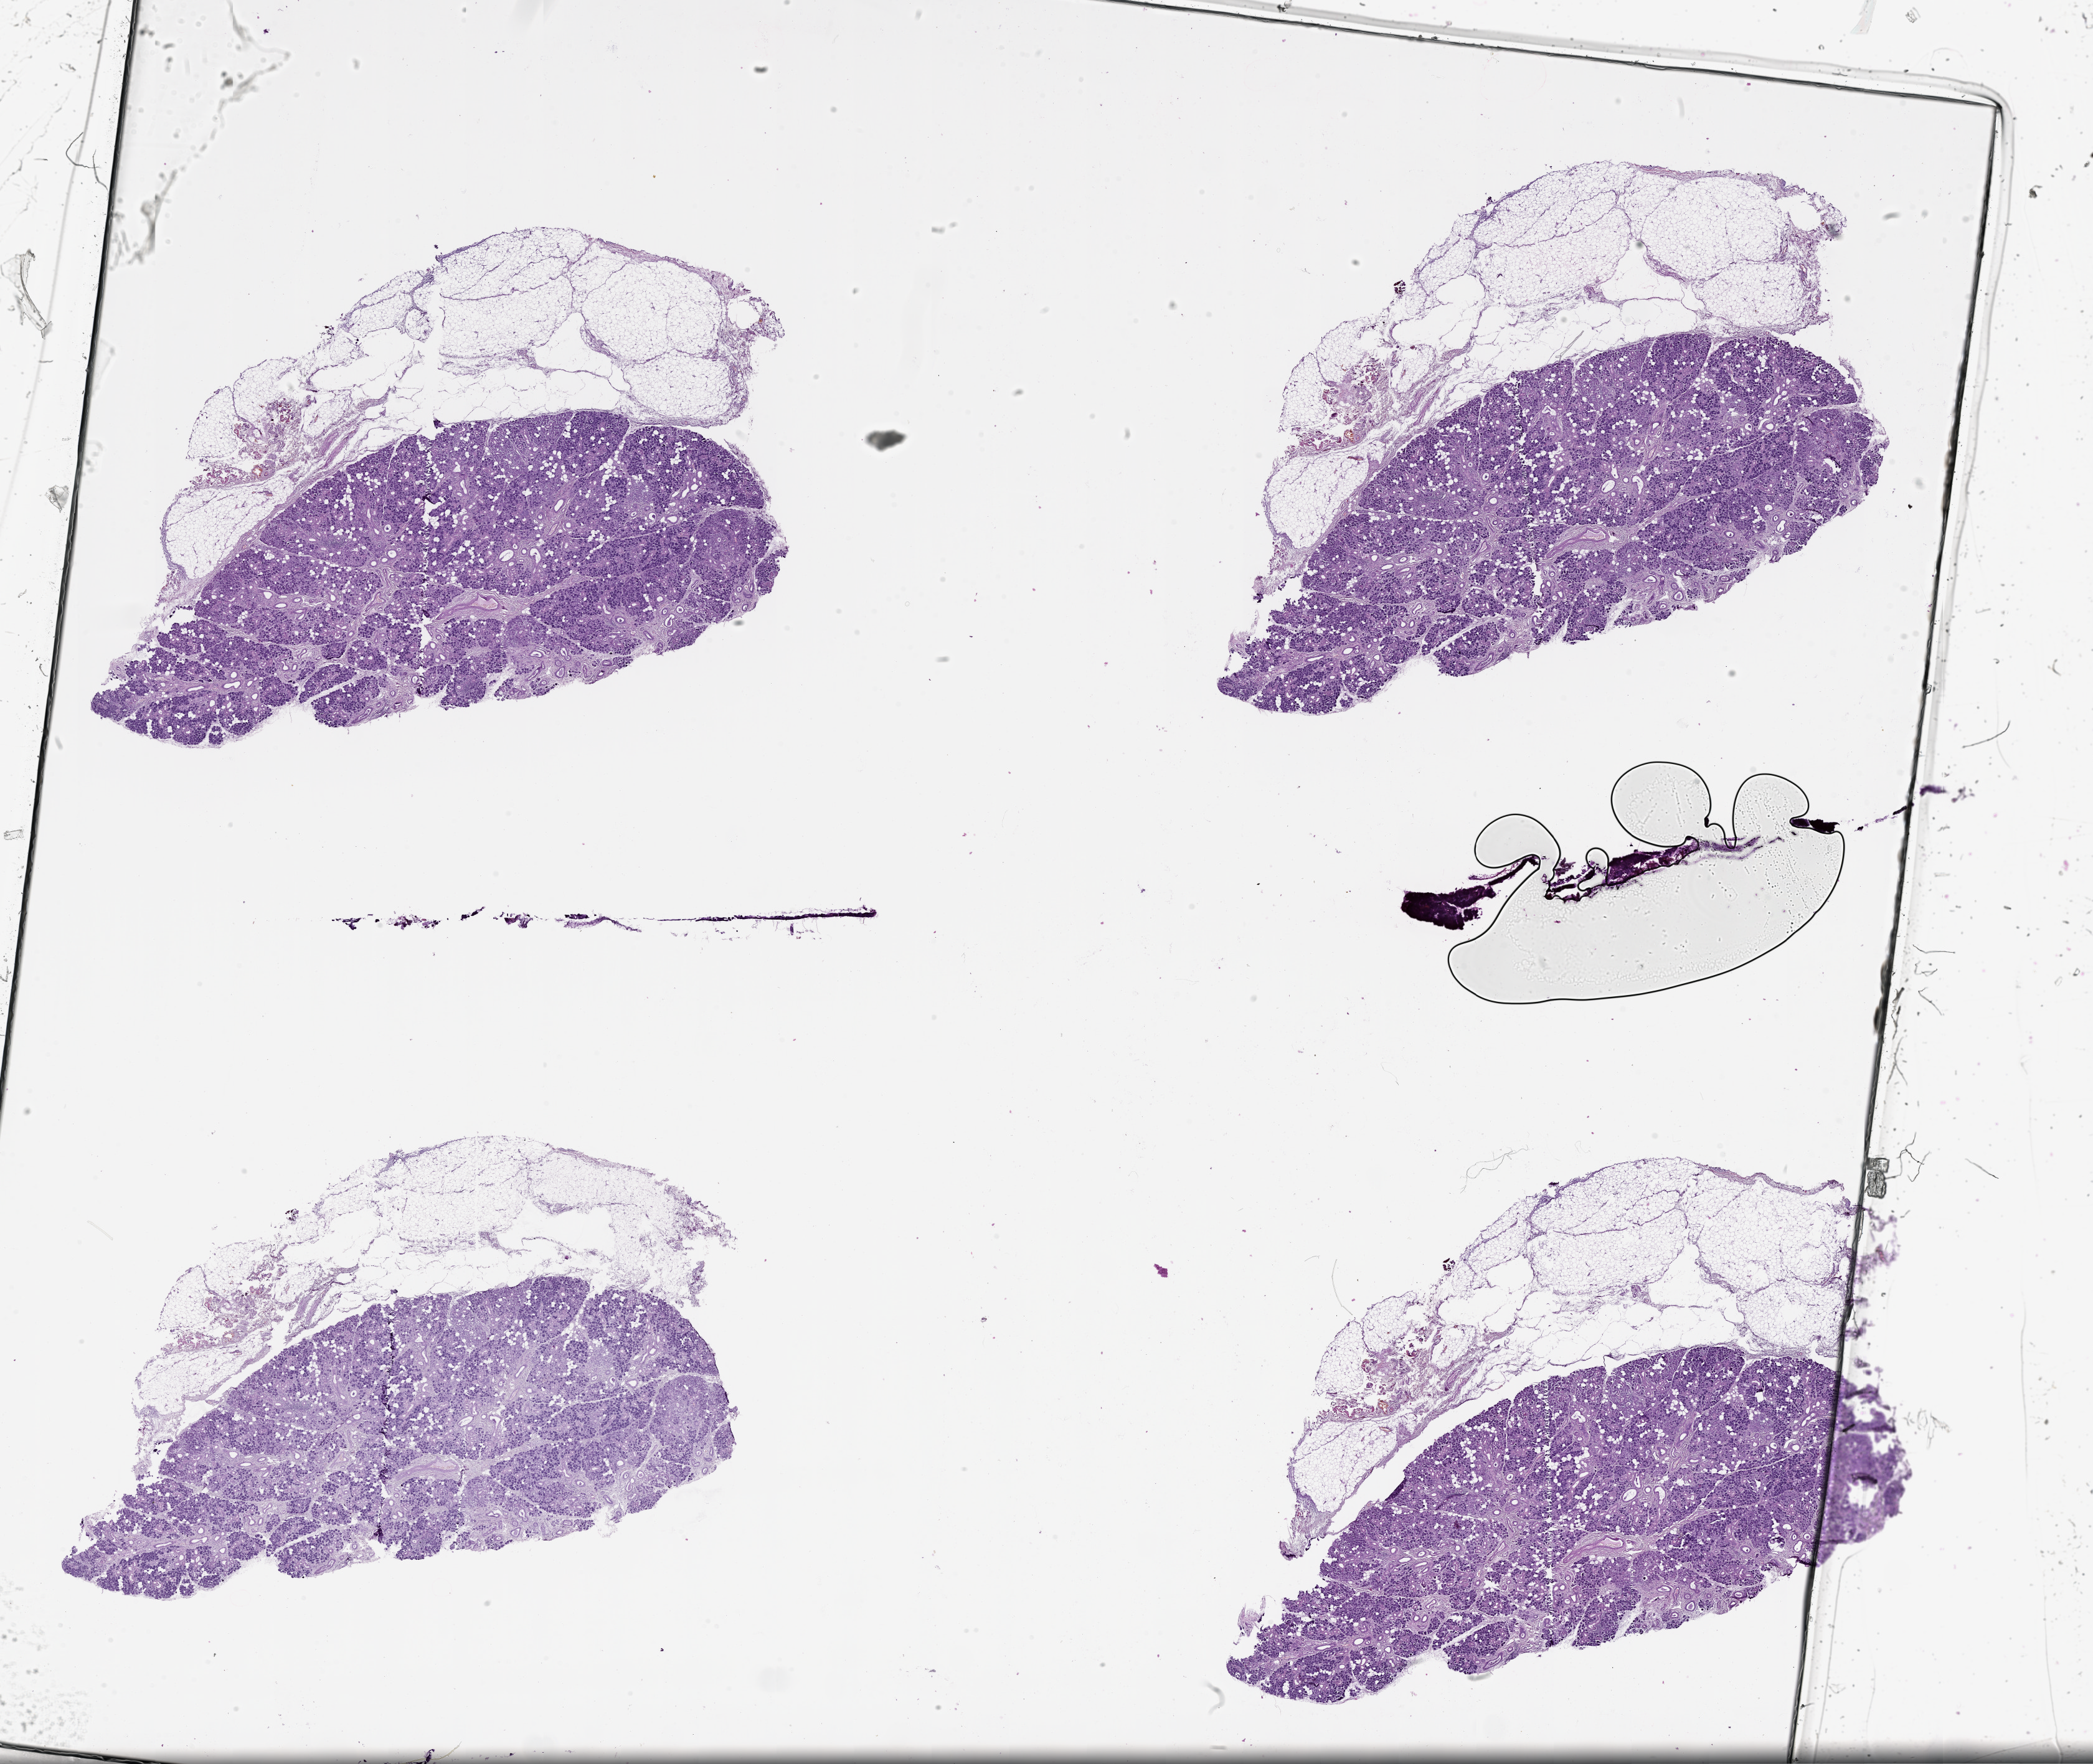
Digitized Hematoxylin and eosin (H&E) stained tissue section (whole slide), whole scanned area (about 27.1 x 22.8 mm, from a 20x scan) shown as a low-resolution overview, head and neck, tissue type not recorded.
Patient diagnosis (cohort enrolment): head and neck cancer (head-neck).